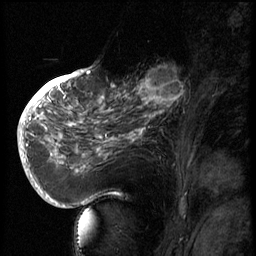
Breast MRI (dynamic contrast-enhanced), one sagittal slice; position 28 of 66 along the scan axis; 3 images stored at this slice position (order not interpretable as contrast timing); 1.5 T; TE 4.2 ms, TR 8.9 ms; 256 × 256 image matrix, field of view 200 × 200 mm. Female patient, age 56 years. Case-level facts recorded for this patient, not image findings: setting: breast cancer imaged before/during neoadjuvant chemotherapy.
Annotated regions visible in this slice (semi-automatically segmented with operator editing):
- analysis volume of interest (the breast-tissue region the enhancement analysis was run in; not a lesion): bounding box (x1, y1, x2, y2) in pixels: (129, 62, 194, 127)
- tumour enhancement mask (voxels above the 140 % enhancement threshold inside the analysis volume of interest): (136, 65, 187, 120)